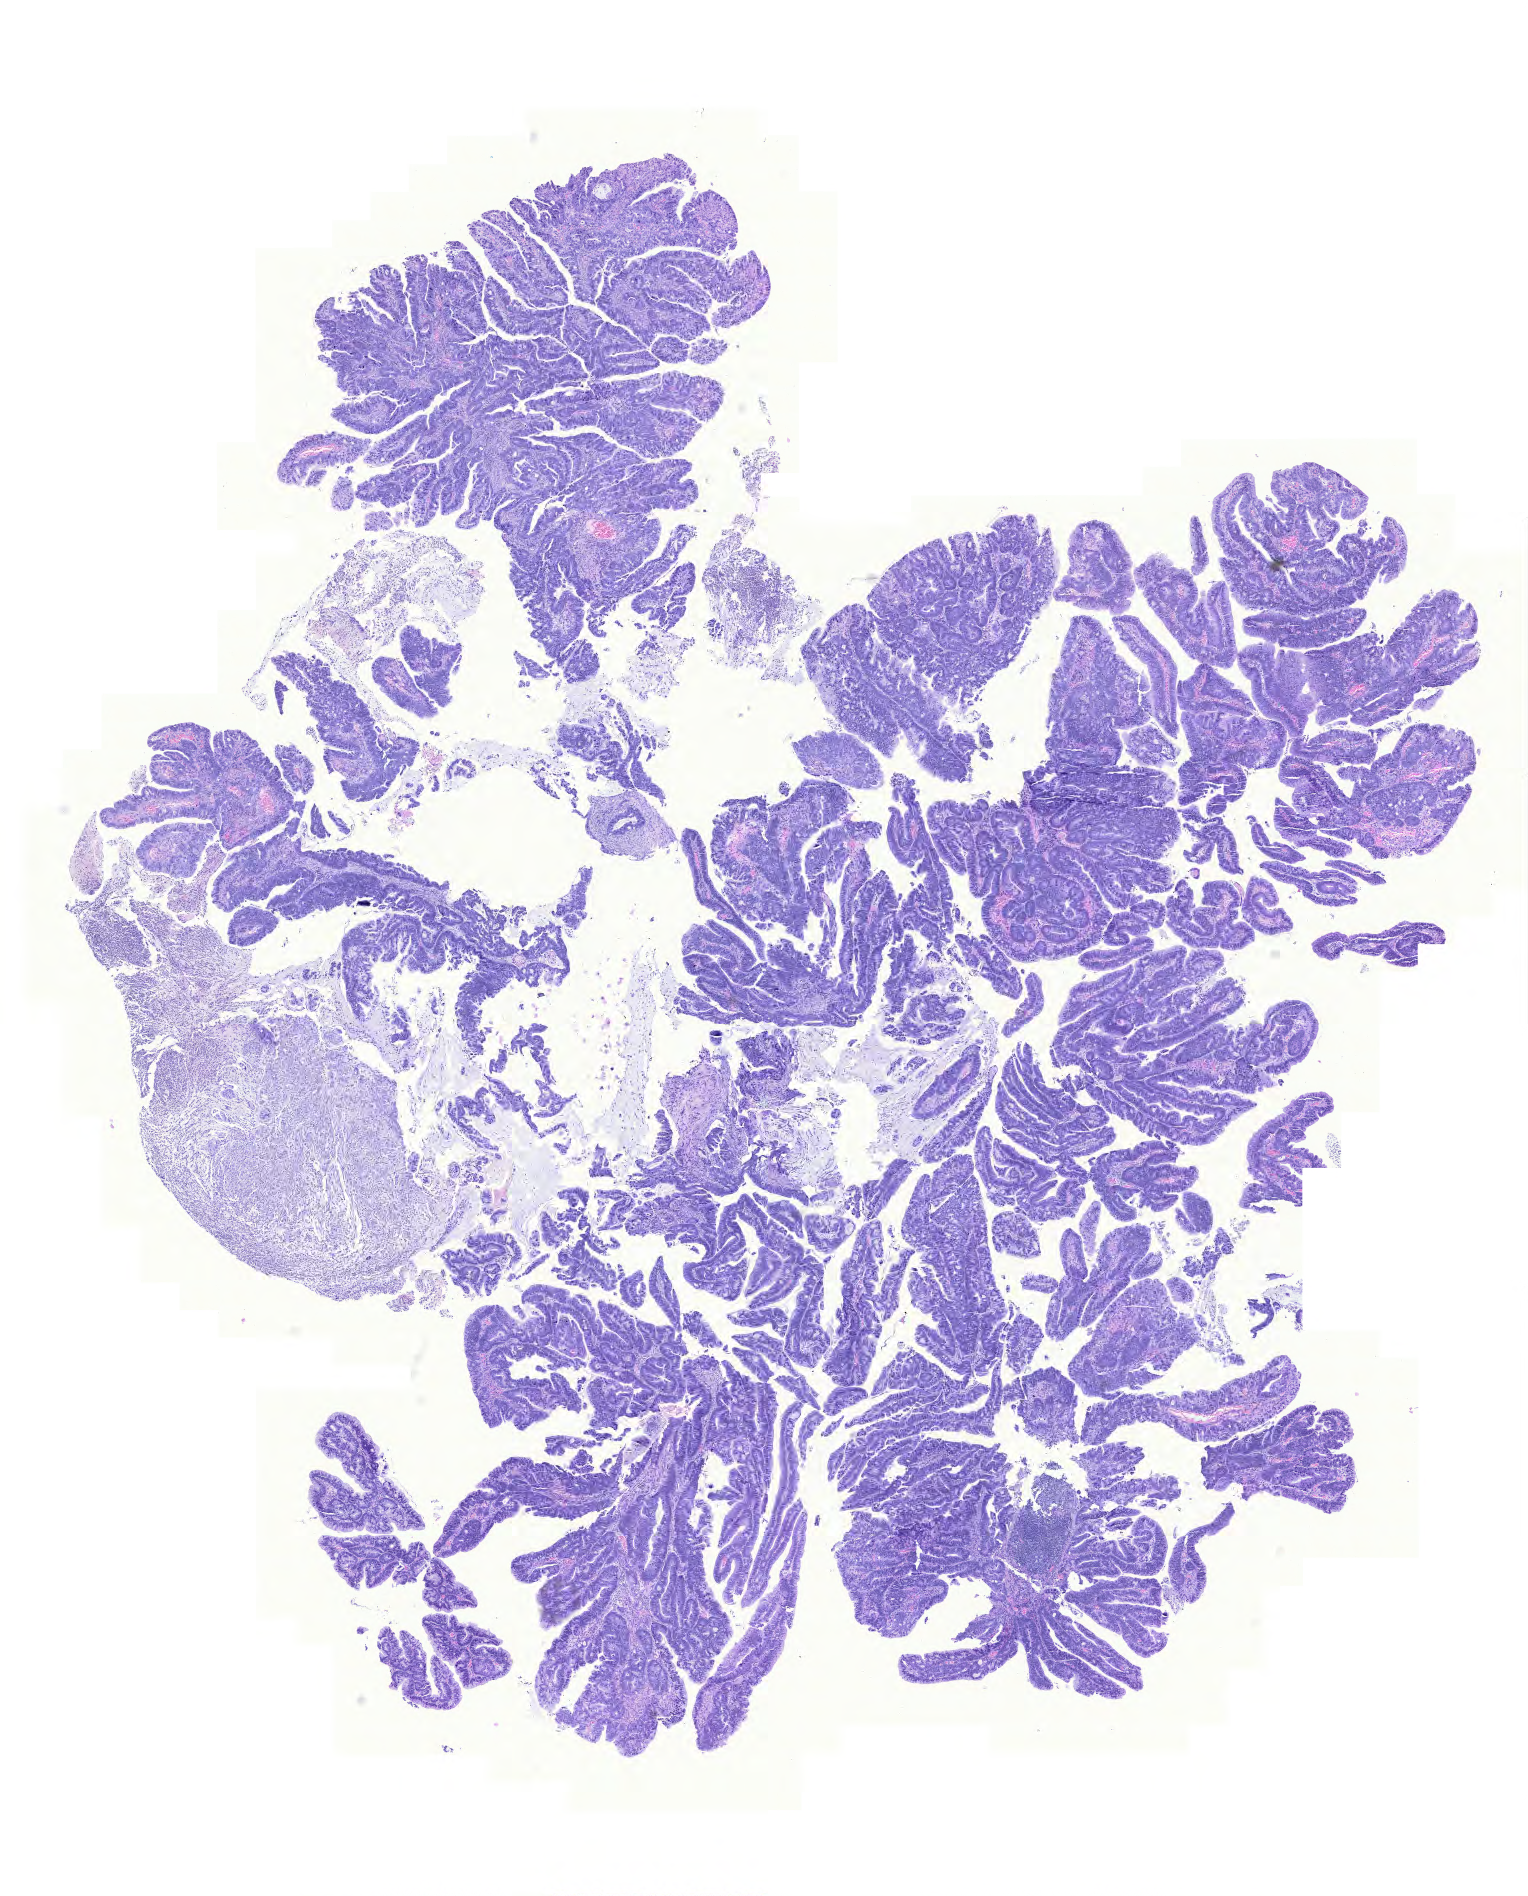
Digitized Hematoxylin and eosin (H&E) stained tissue section (whole slide), a low-resolution overview of the entire scanned area, about 11.4 x 14.1 mm (acquisition: 20x scan); FFPE section; rectum, primary tumour sample. Patient: female, age at initial diagnosis 76 years.
Lymph nodes positive (case pathology): 0 of 25 examined. AJCC pathologic stage: IIA (6th edition). Histologic diagnosis: Mucinous adenocarcinoma (rectosigmoid junction).